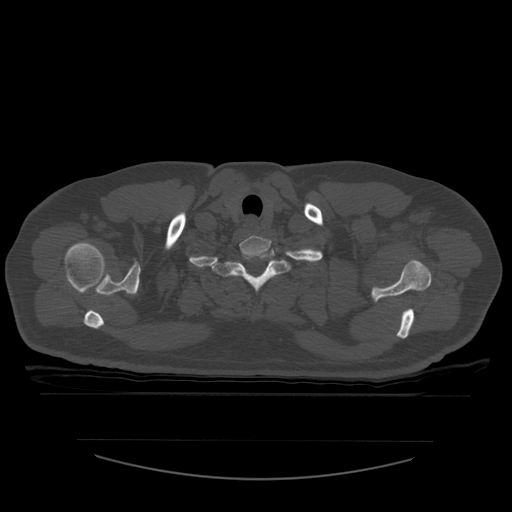
CT including the spine, one axial slice; position 471 of 532 along the scan axis; 120 kVp; bone window (W 1800 / L 400 HU); 1.25 mm slice thickness; 512 × 512 image matrix, field of view 441 × 441 mm. Patient age 44 years. From the clinical record (not read from this slice): primary cancer: soft tissue sarcoma.
Outlined on this slice (semi-automatically segmented with operator editing):
- T1 vertebra: box from (x=211, y=247) to (x=297, y=292) px